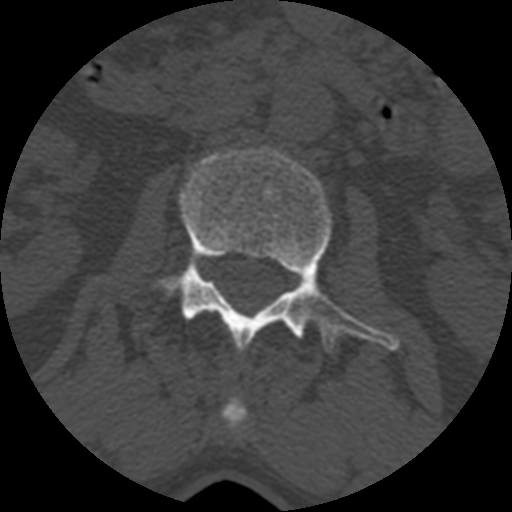
CT including the spine, one axial slice. Position 334 of 399 along the scan axis. 120 kVp. Bone window (W 1800 / L 400 HU). 512 × 512 image matrix, field of view 160 × 160 mm. Patient age 71 years. From the clinical record (not read from this slice): primary cancer: prostate.
Structures marked on this image (semi-automatically segmented with operator editing):
- L1 vertebra: bounding box <220,398,246,428> (left, top, right, bottom; pixels)
- L2 vertebra: <156,147,399,353>